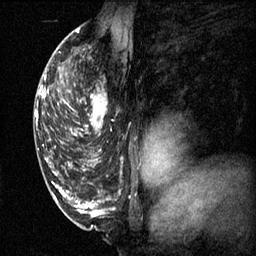
Breast MRI (dynamic contrast-enhanced), one sagittal slice; slice 35 of 60 in the series (ordered by position); 3 images stored at this slice position (order not interpretable as contrast timing); 1.5 T; TE 4.2 ms, TR 11.1 ms; 2 mm slice thickness; 256 × 256 image matrix, field of view 180 × 180 mm. Female patient, age 50 years.
Structures marked on this image (semi-automatic segmentation, software-assisted and operator-edited):
- analysis volume of interest (the breast-tissue region the enhancement analysis was run in; not a lesion): bounding box <68,68,114,141> (left, top, right, bottom; pixels)
- tumour enhancement mask (voxels above the 70 % enhancement threshold inside the analysis volume of interest): <68,94,108,137>